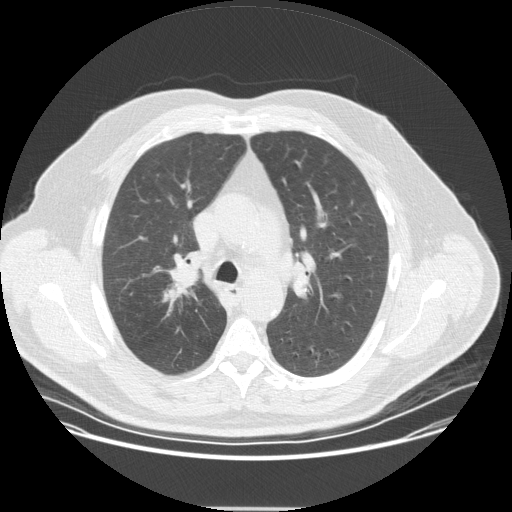
Chest CT (low-dose screening protocol), one axial image. Second annual screen. Lung window (W 1500 / L -600 HU). 2.5 mm slice thickness. Standard (soft-tissue) reconstruction kernel (STANDARD). 512 × 512 image matrix. Male participant, aged 57 years at enrolment.
- Expert-annotated lung lesion, bounding box [x1, y1, x2, y2] px = [147, 250, 211, 311].
- Reader record for this screening exam (exam-level; its link to the box is not recorded): non-calcified nodule or mass ≥4 mm, right upper lobe, 20 × 16 mm, spiculated (stellate) margins, soft tissue attenuation, pre-existing on the prior screen: no.
- Official screen result: positive, other.